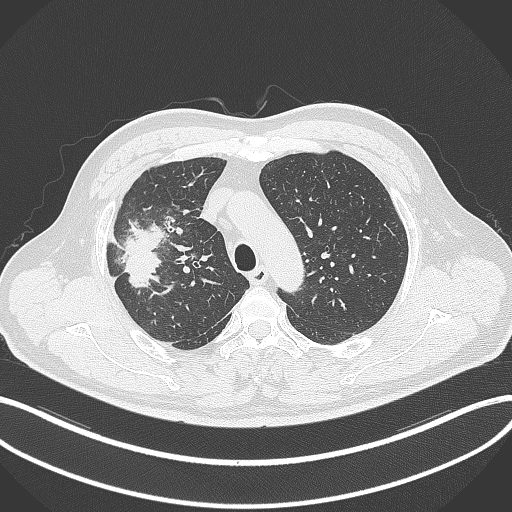
Chest CT, one axial slice. Position 255 of 348 along the scan axis. Lung window (W 1500 / L -600 HU). 512 × 512 image matrix, field of view 400 × 400 mm. Patient: male, 55 years. Case-level facts recorded for this patient, not image findings: clinical TNM (as recorded): T3 N2 M1.
Annotated regions visible in this slice (rectangle marked by the reading radiologist):
- lung tumour (recorded histology: adenocarcinoma): box from (x=116, y=215) to (x=167, y=295) px